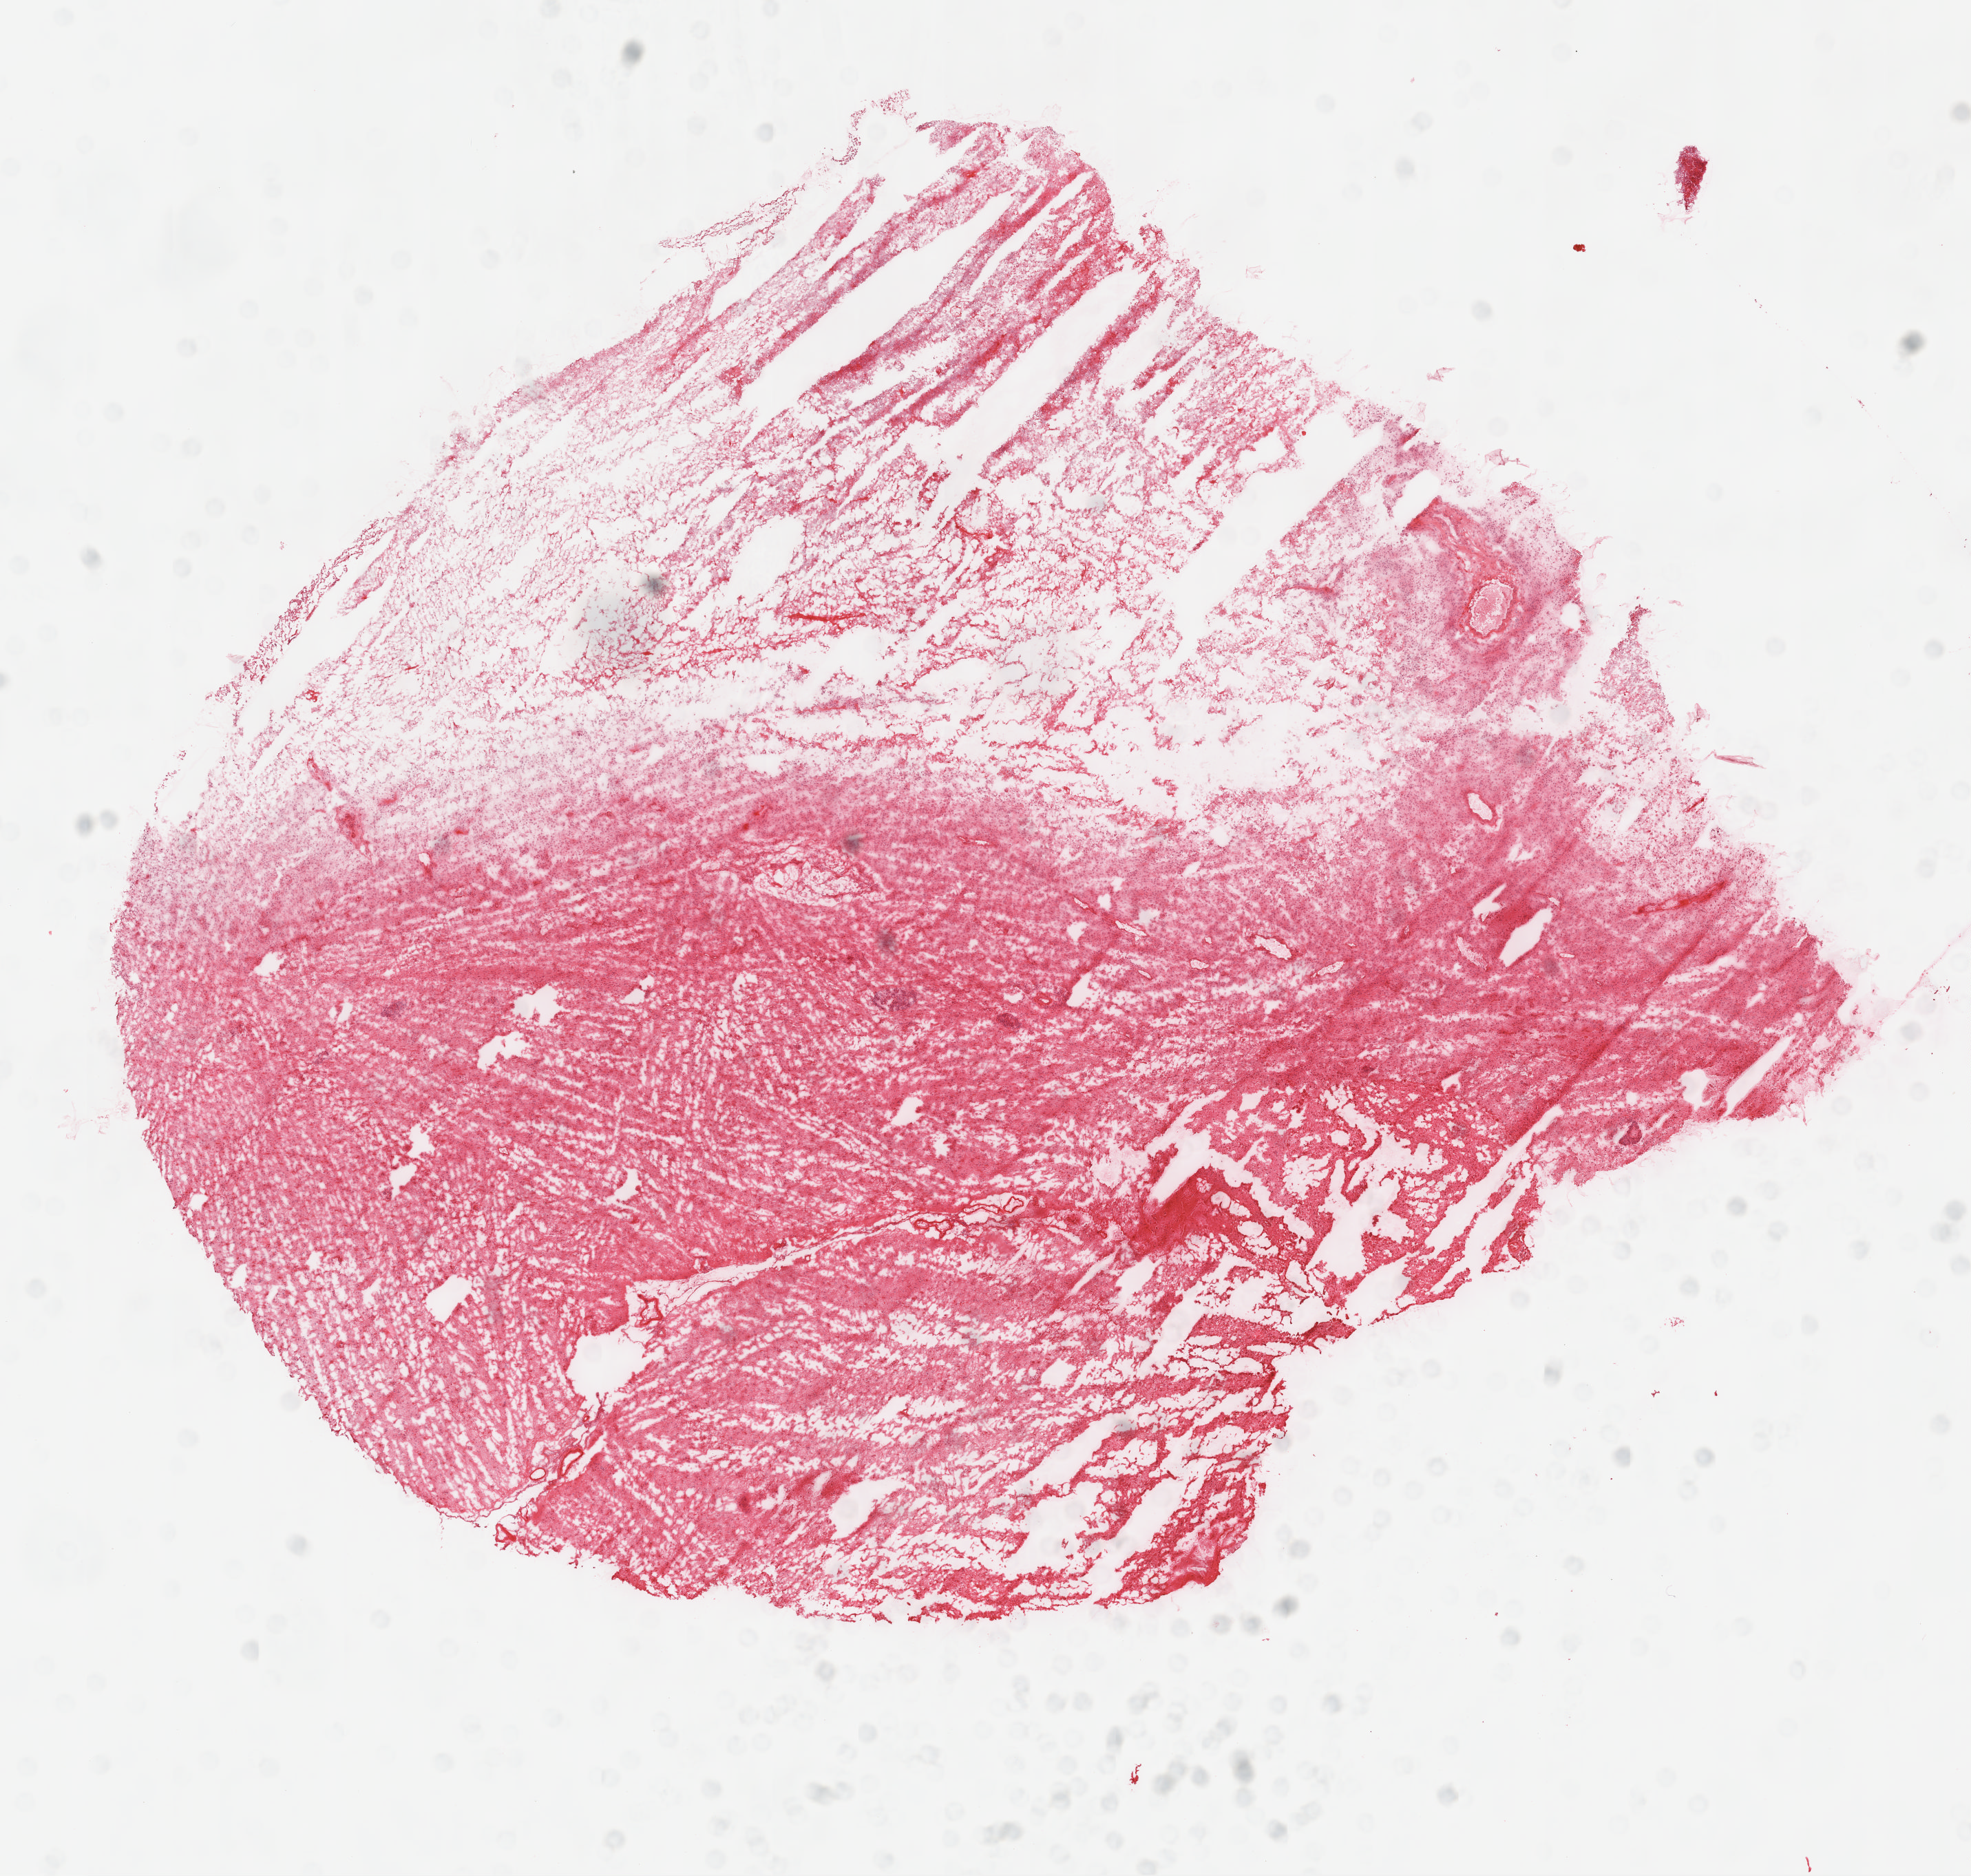
Digitized Hematoxylin and eosin (H&E) stained tissue section (whole slide), whole scanned area (about 11.6 x 11.0 mm, acquisition: 40x scan) shown as a low-resolution overview. Frozen section from the top of the tissue portion. Sample: primary tumour, brain. Male, age 75 years at initial diagnosis. Pathologist review of this section (percent, as recorded): tumour cells 90%, tumour nuclei 100%, normal cells 0%, stromal cells 0%, necrosis 10%.
- diagnosis: Glioblastoma